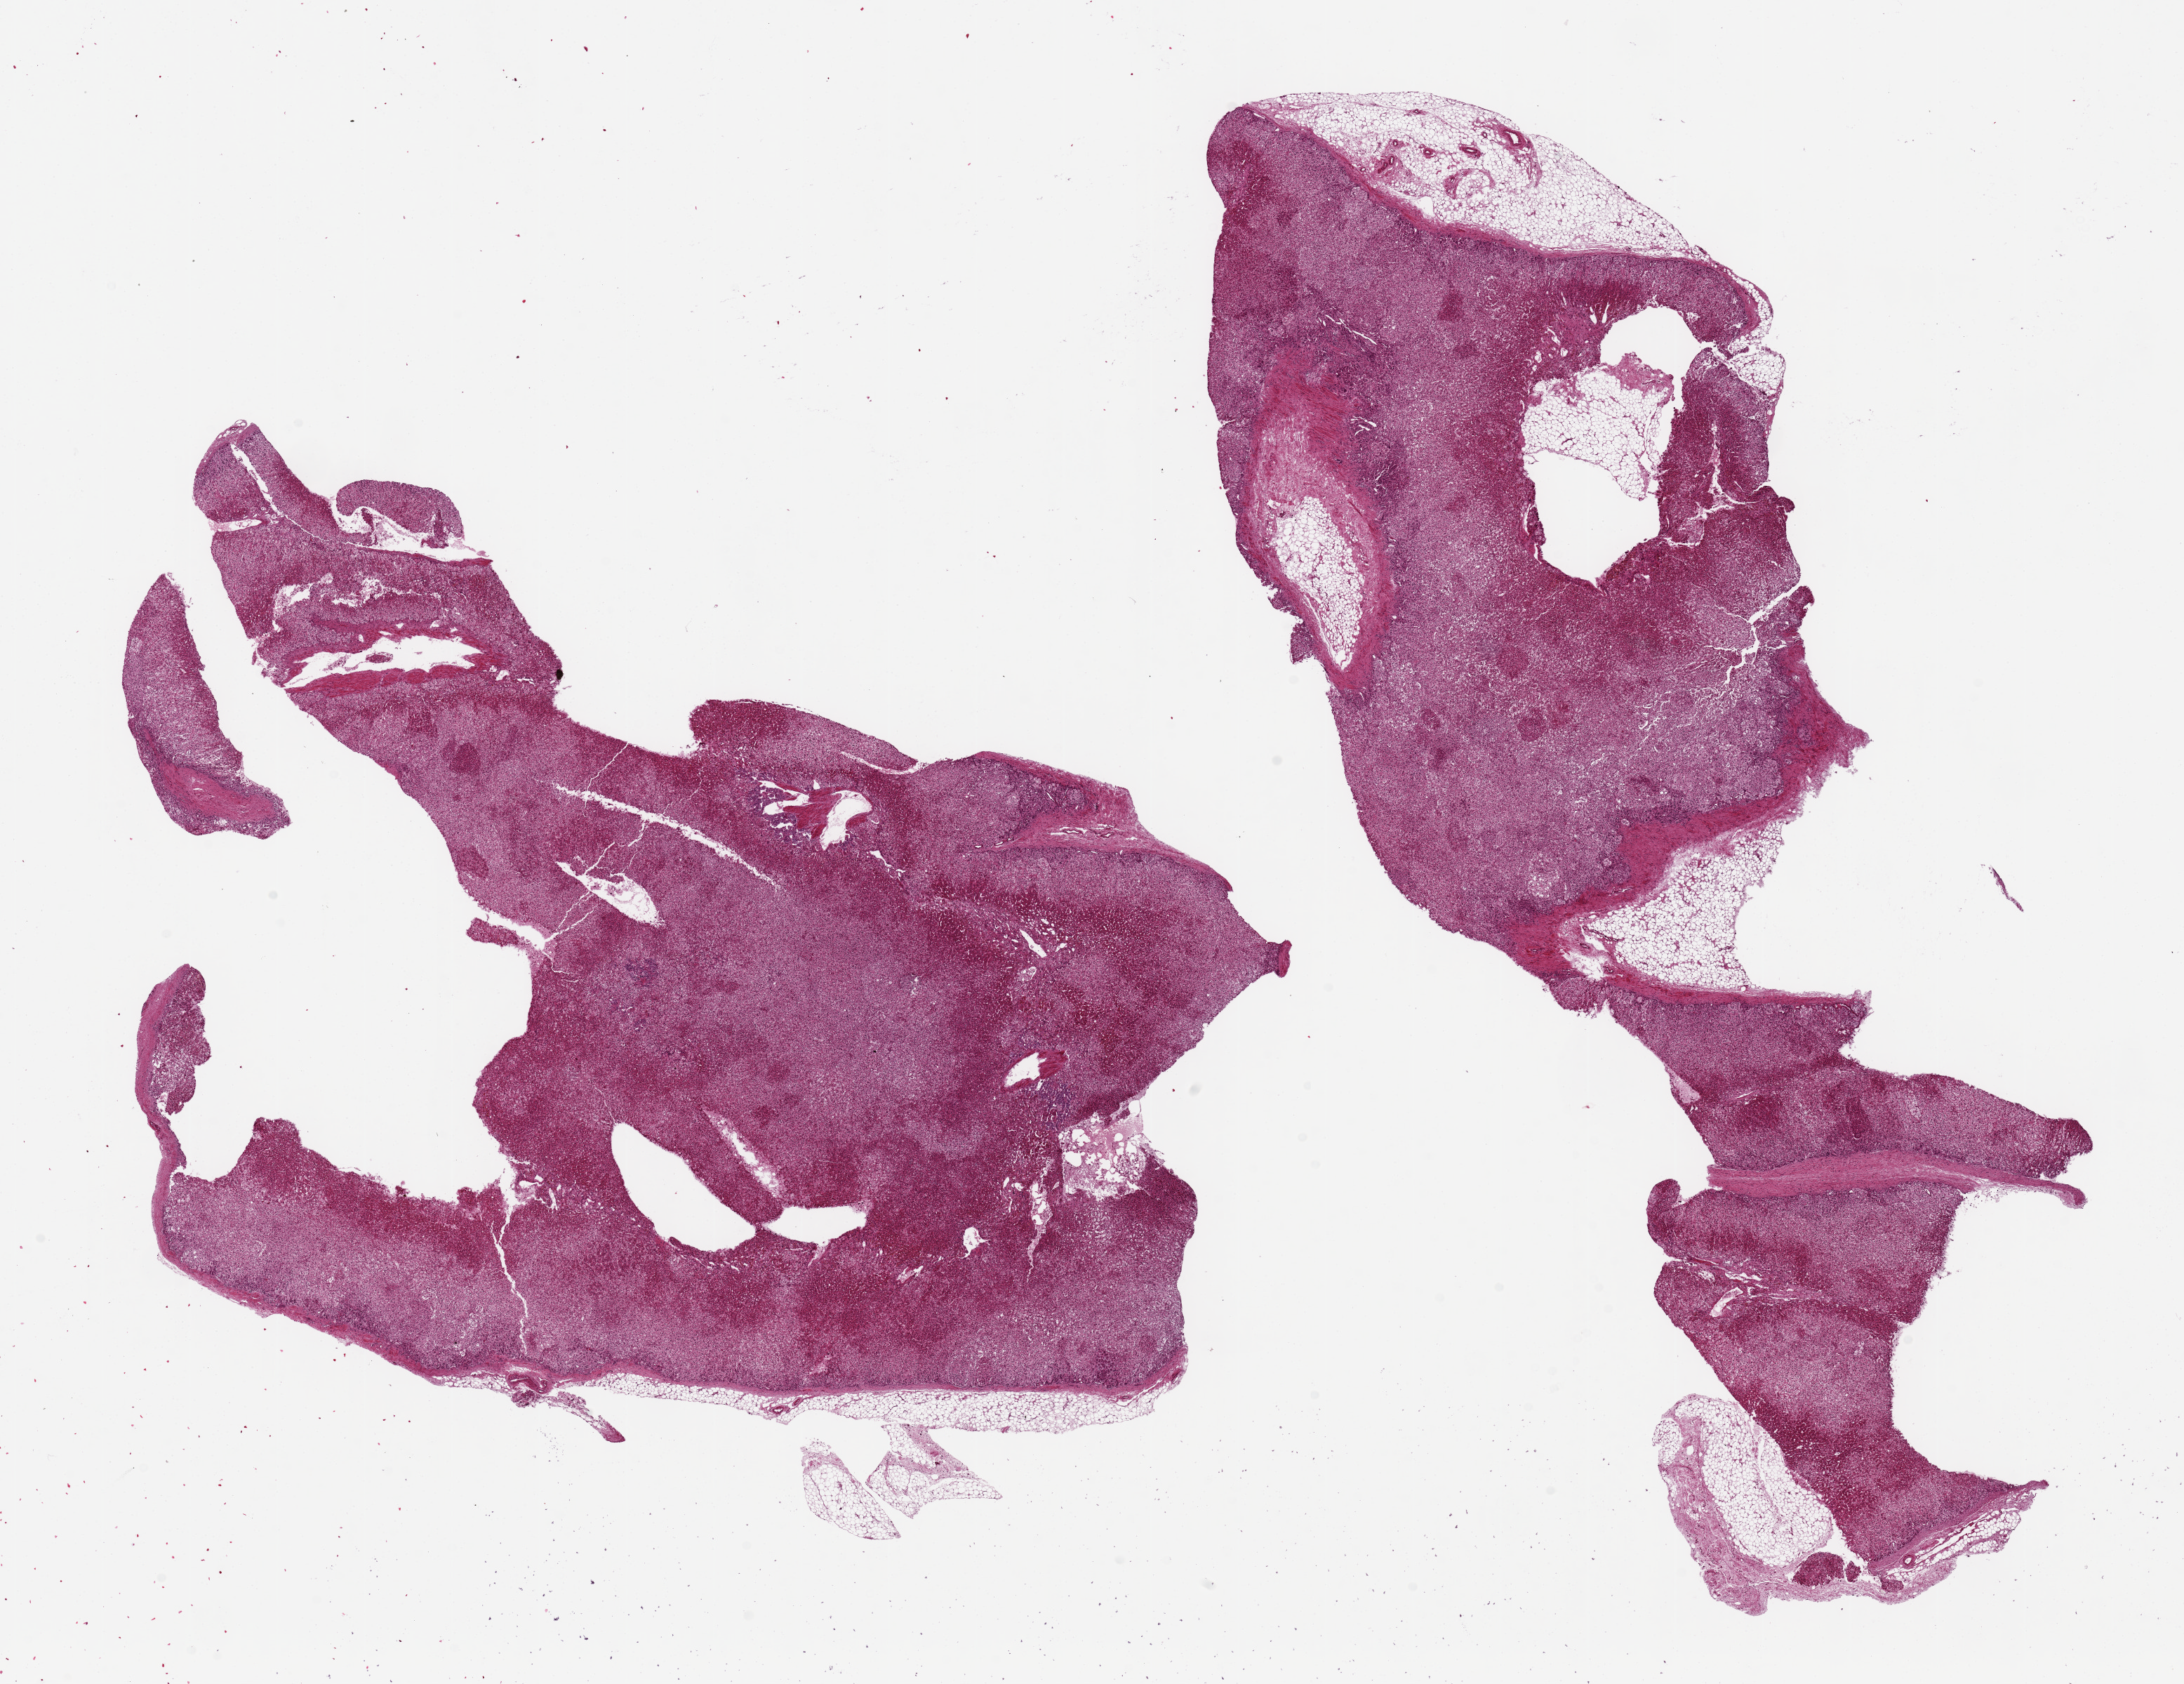
Whole-slide image, hematoxylin and eosin (H&E) stain — a low-resolution overview of the entire scanned area, about 24.6 x 19.0 mm (slide scanned at 20x); PAXgene-fixed, paraffin-embedded tissue; section of adrenal gland (target tissue); tissue donor sample. Donor: male.
* reviewer comment on this tissue sample: 2 pieces 18x5 & 12x9 mm; cortex; ~20% adipose